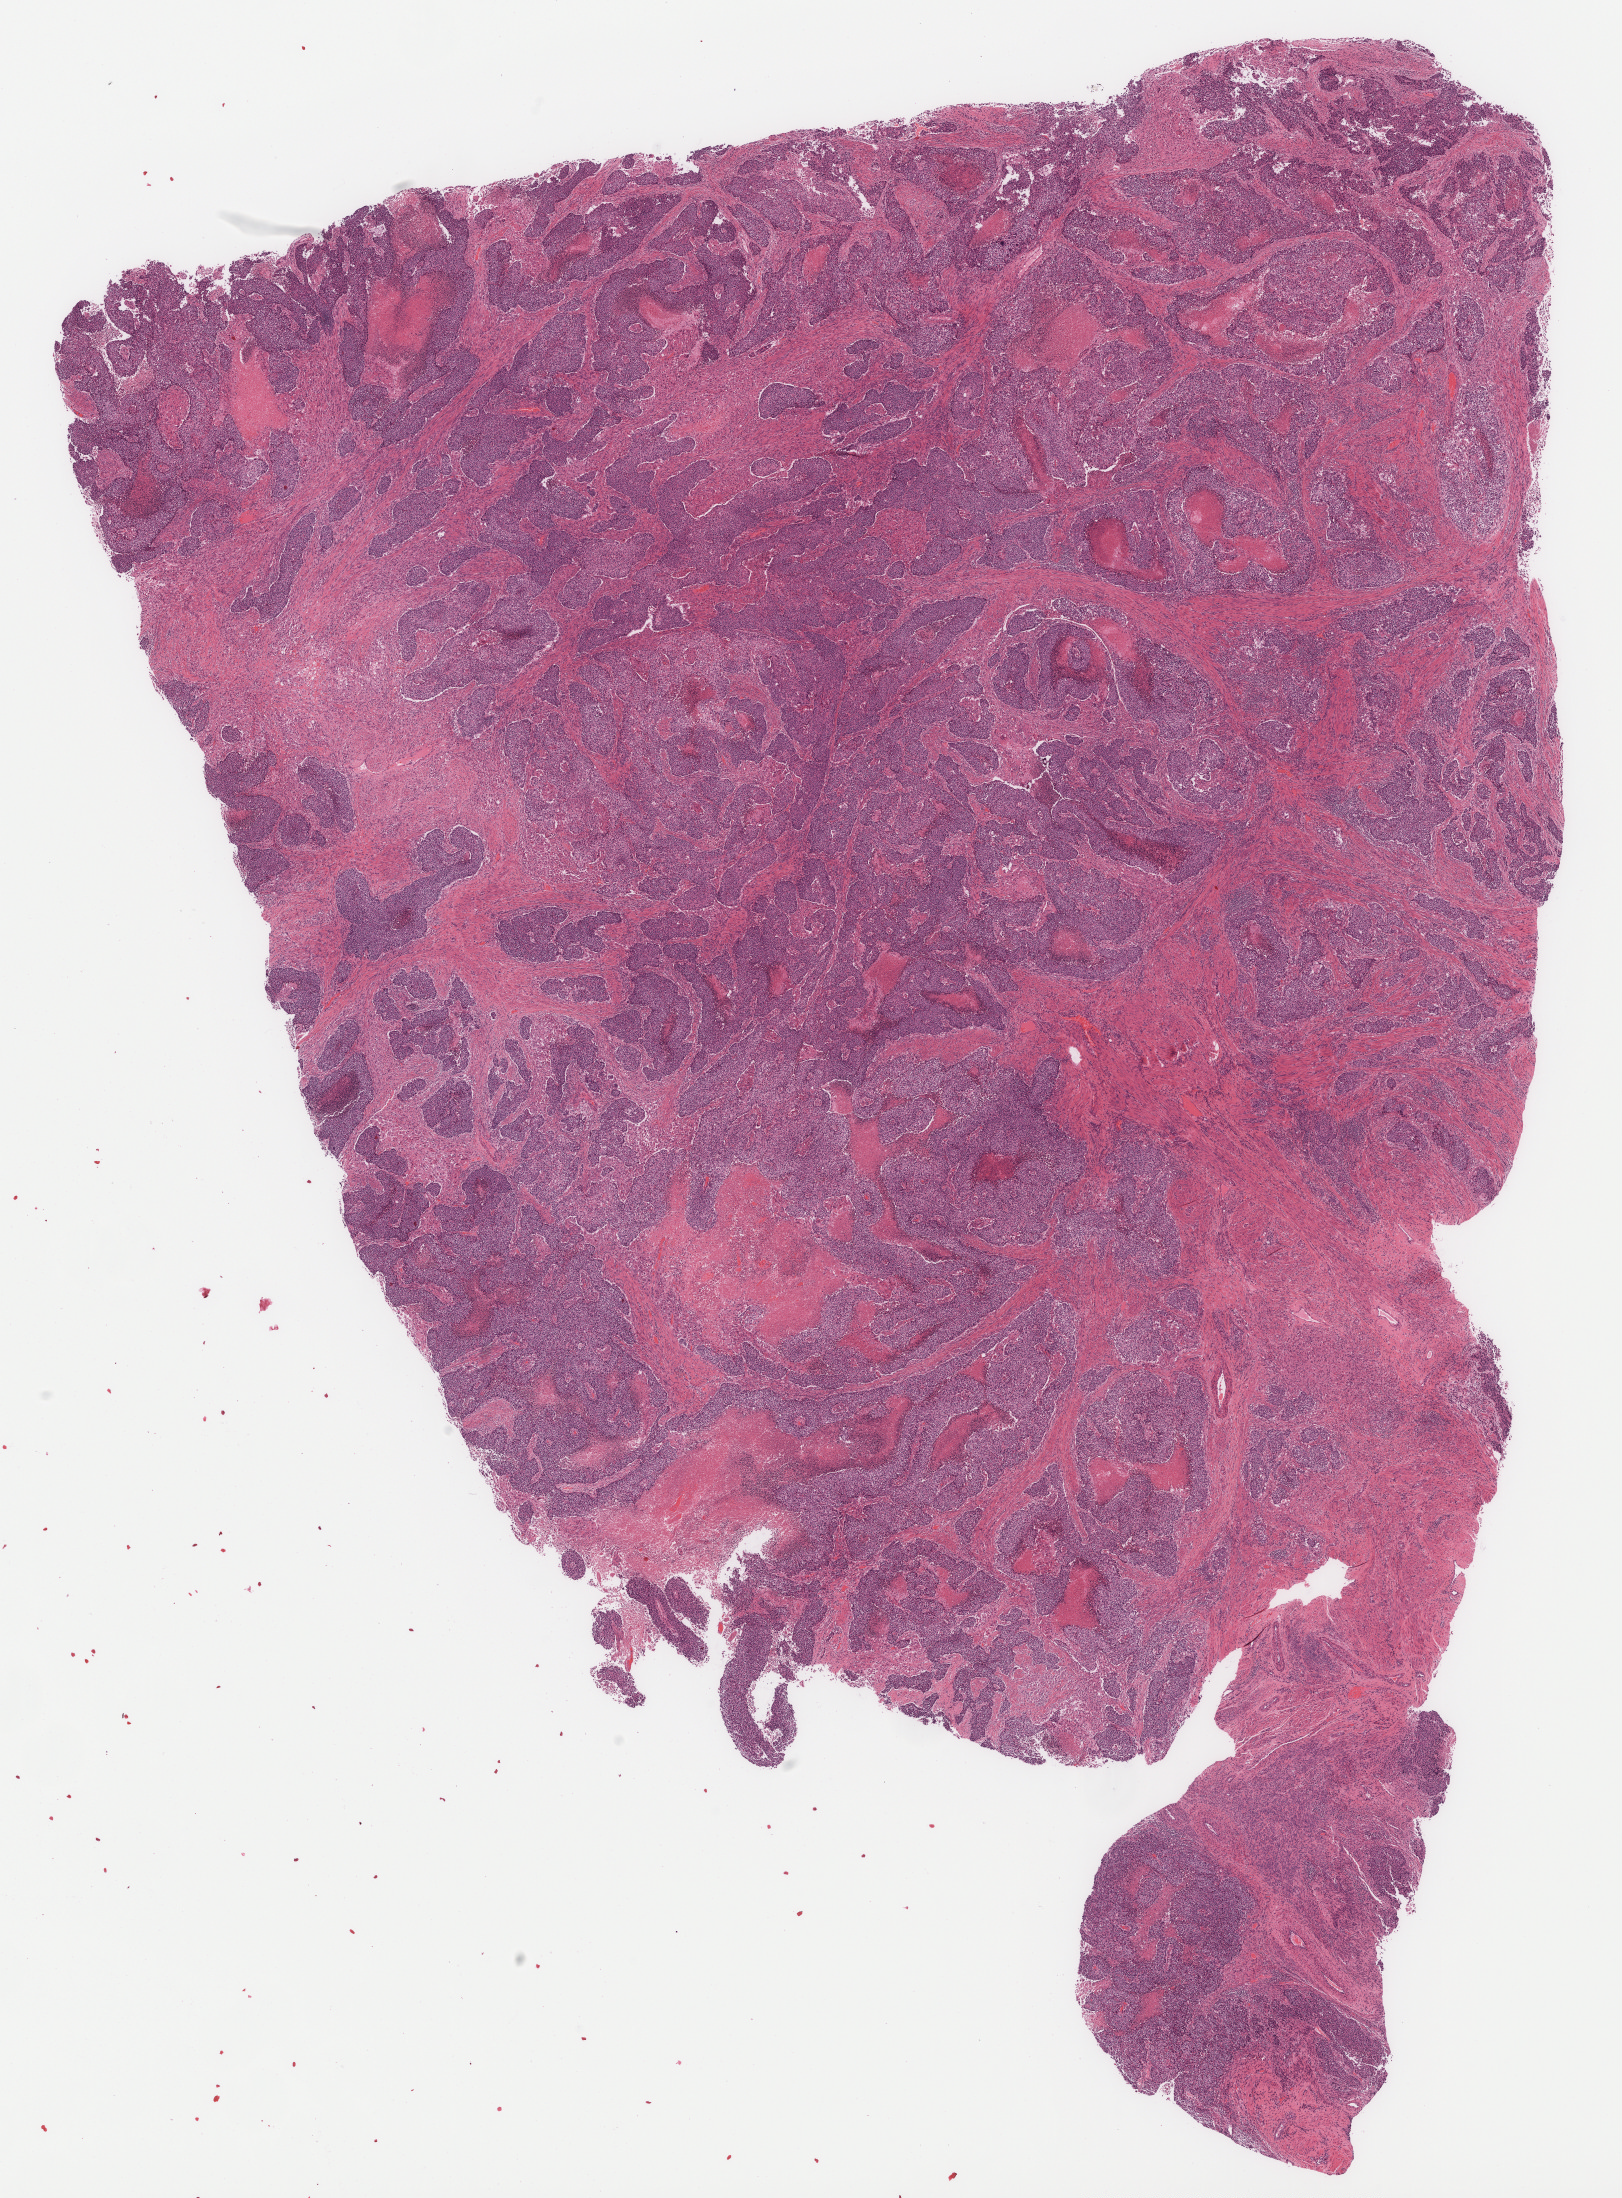
Digitized H&E-stained tissue section (whole slide) — whole scanned area (about 13.1 x 17.7 mm) shown as a low-resolution overview, formalin-fixed paraffin-embedded (FFPE) diagnostic section, uterus, primary tumour sample. Female patient; age at initial diagnosis 43 years. Histologic grade: G3 (poorly differentiated).
* FIGO stage: IIIC2
* histologic diagnosis: Endometrioid adenocarcinoma, NOS (endometrium)